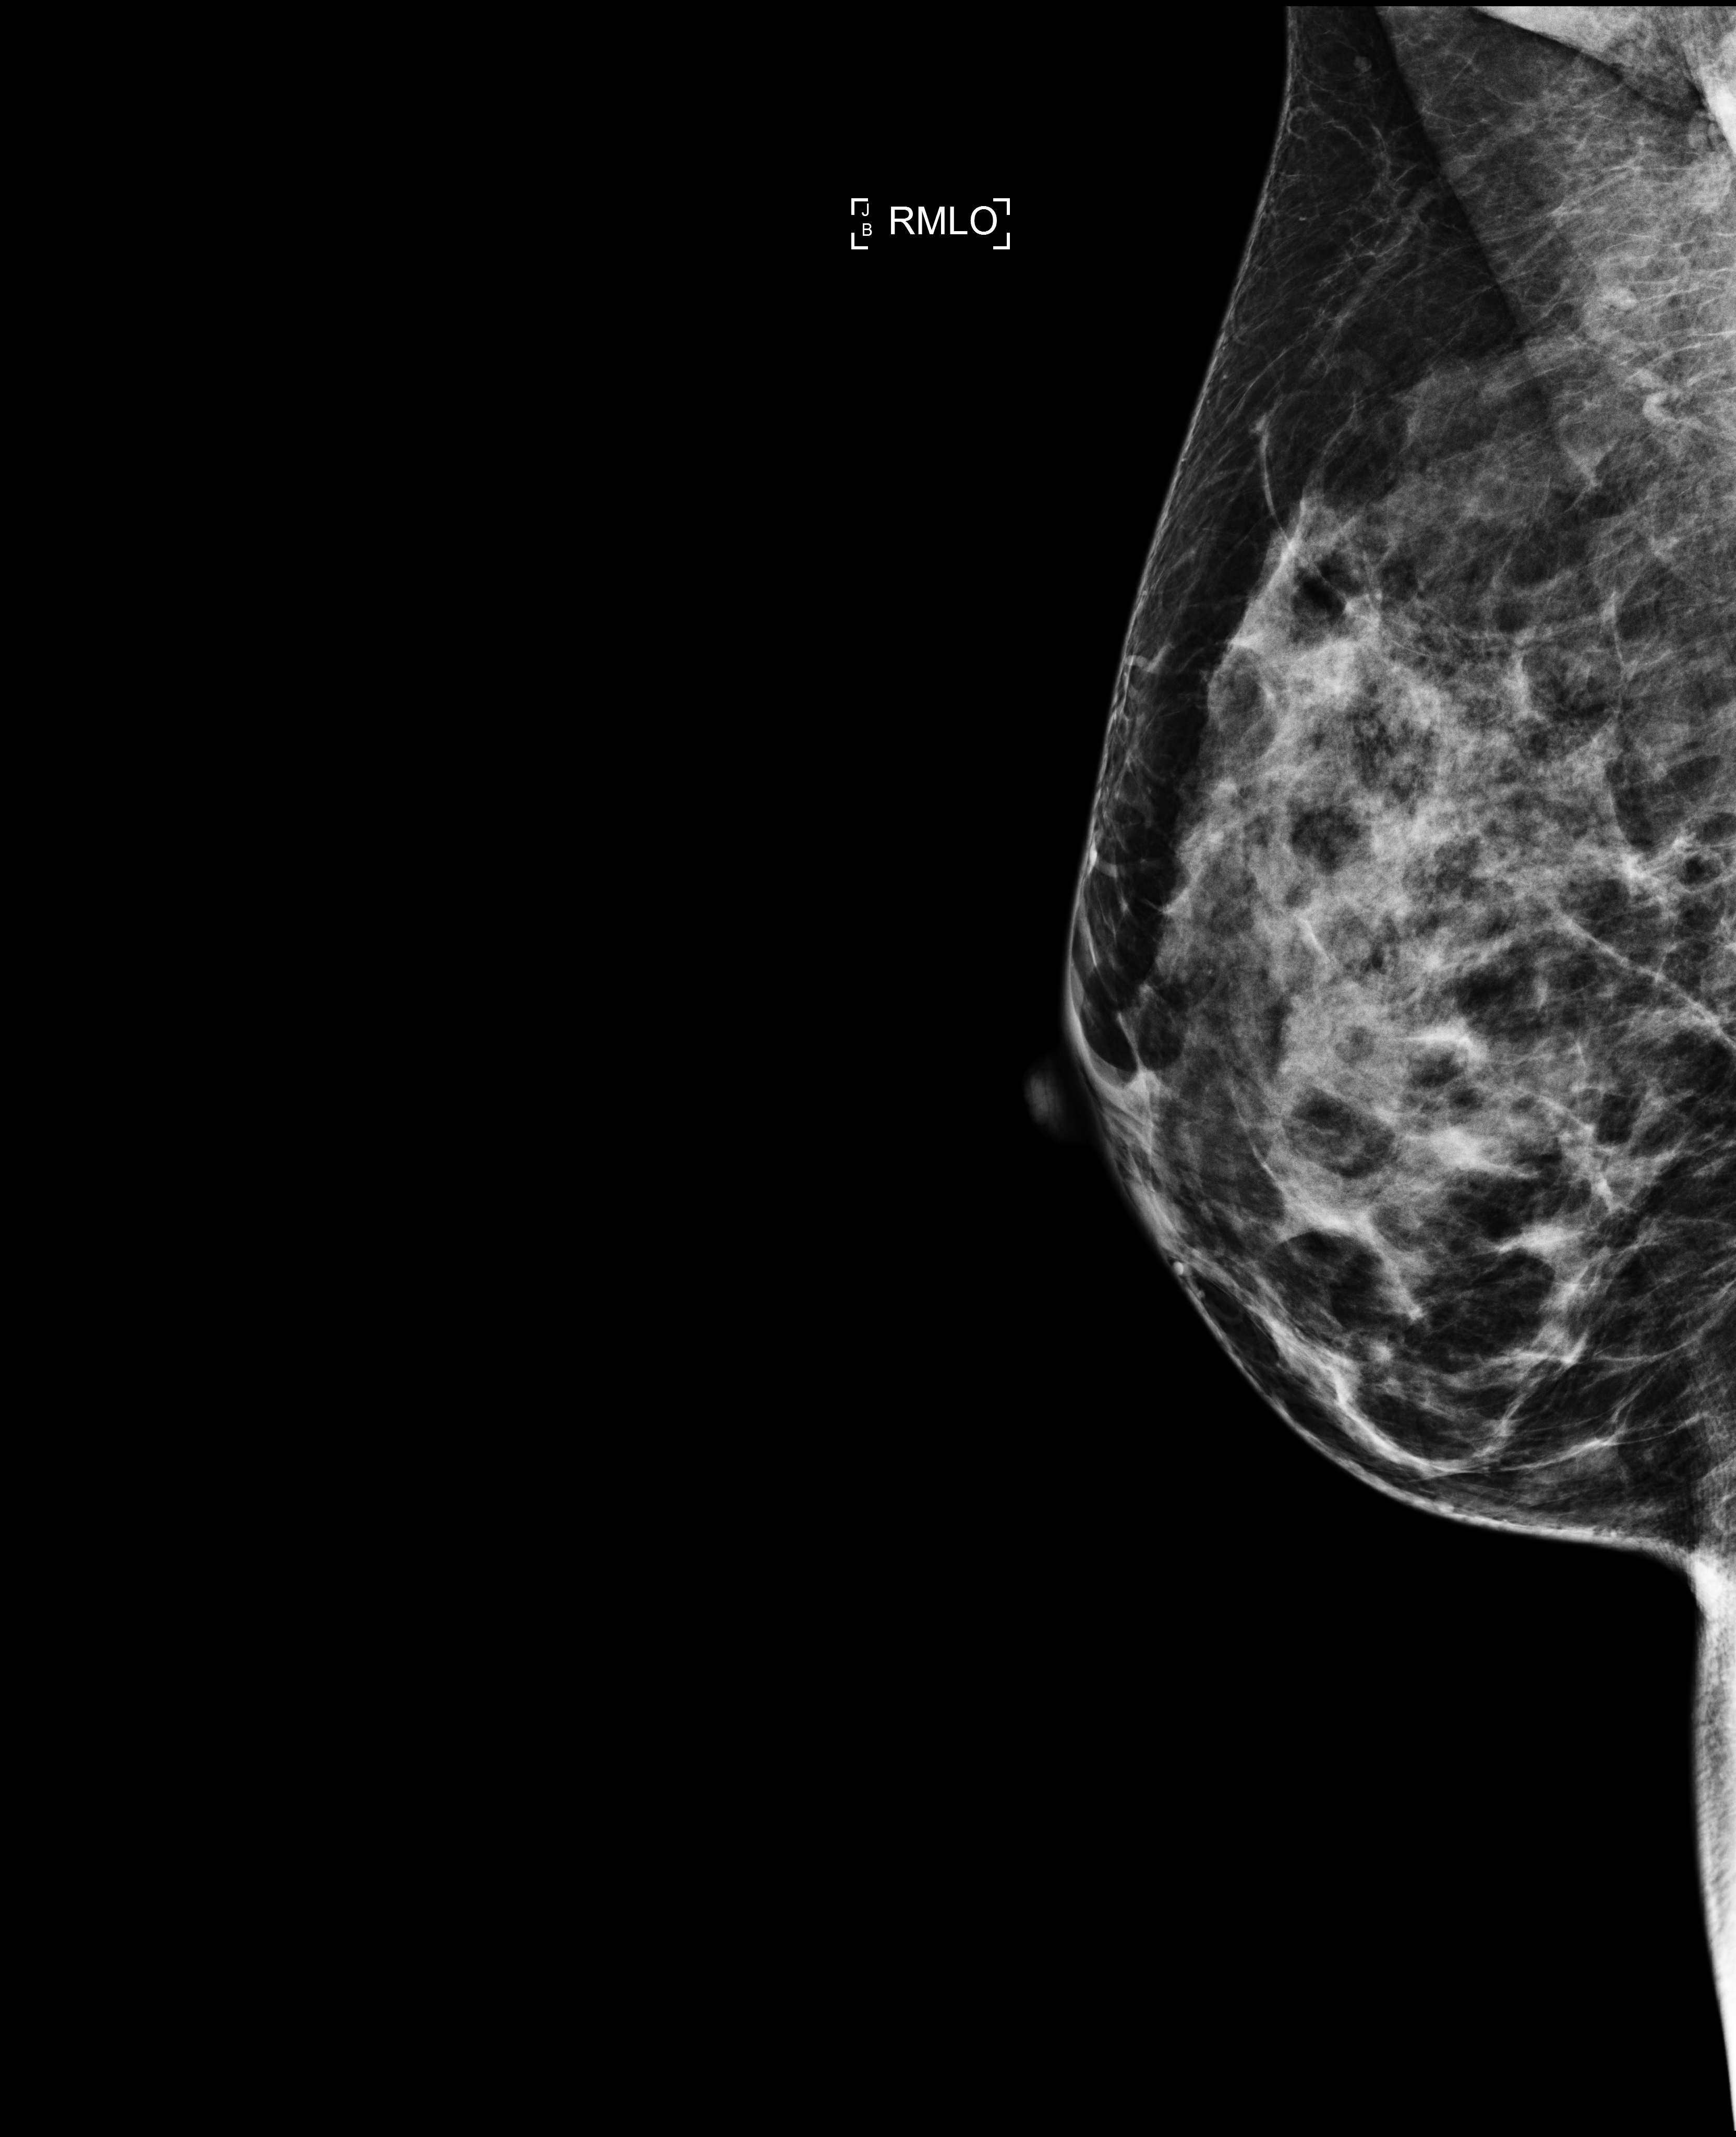
Screening examination; compressed breast thickness 61 mm. Patient: female, 42 years.
Image type: full-field digital mammogram. Breast: right. Projection: medio-lateral oblique projection.